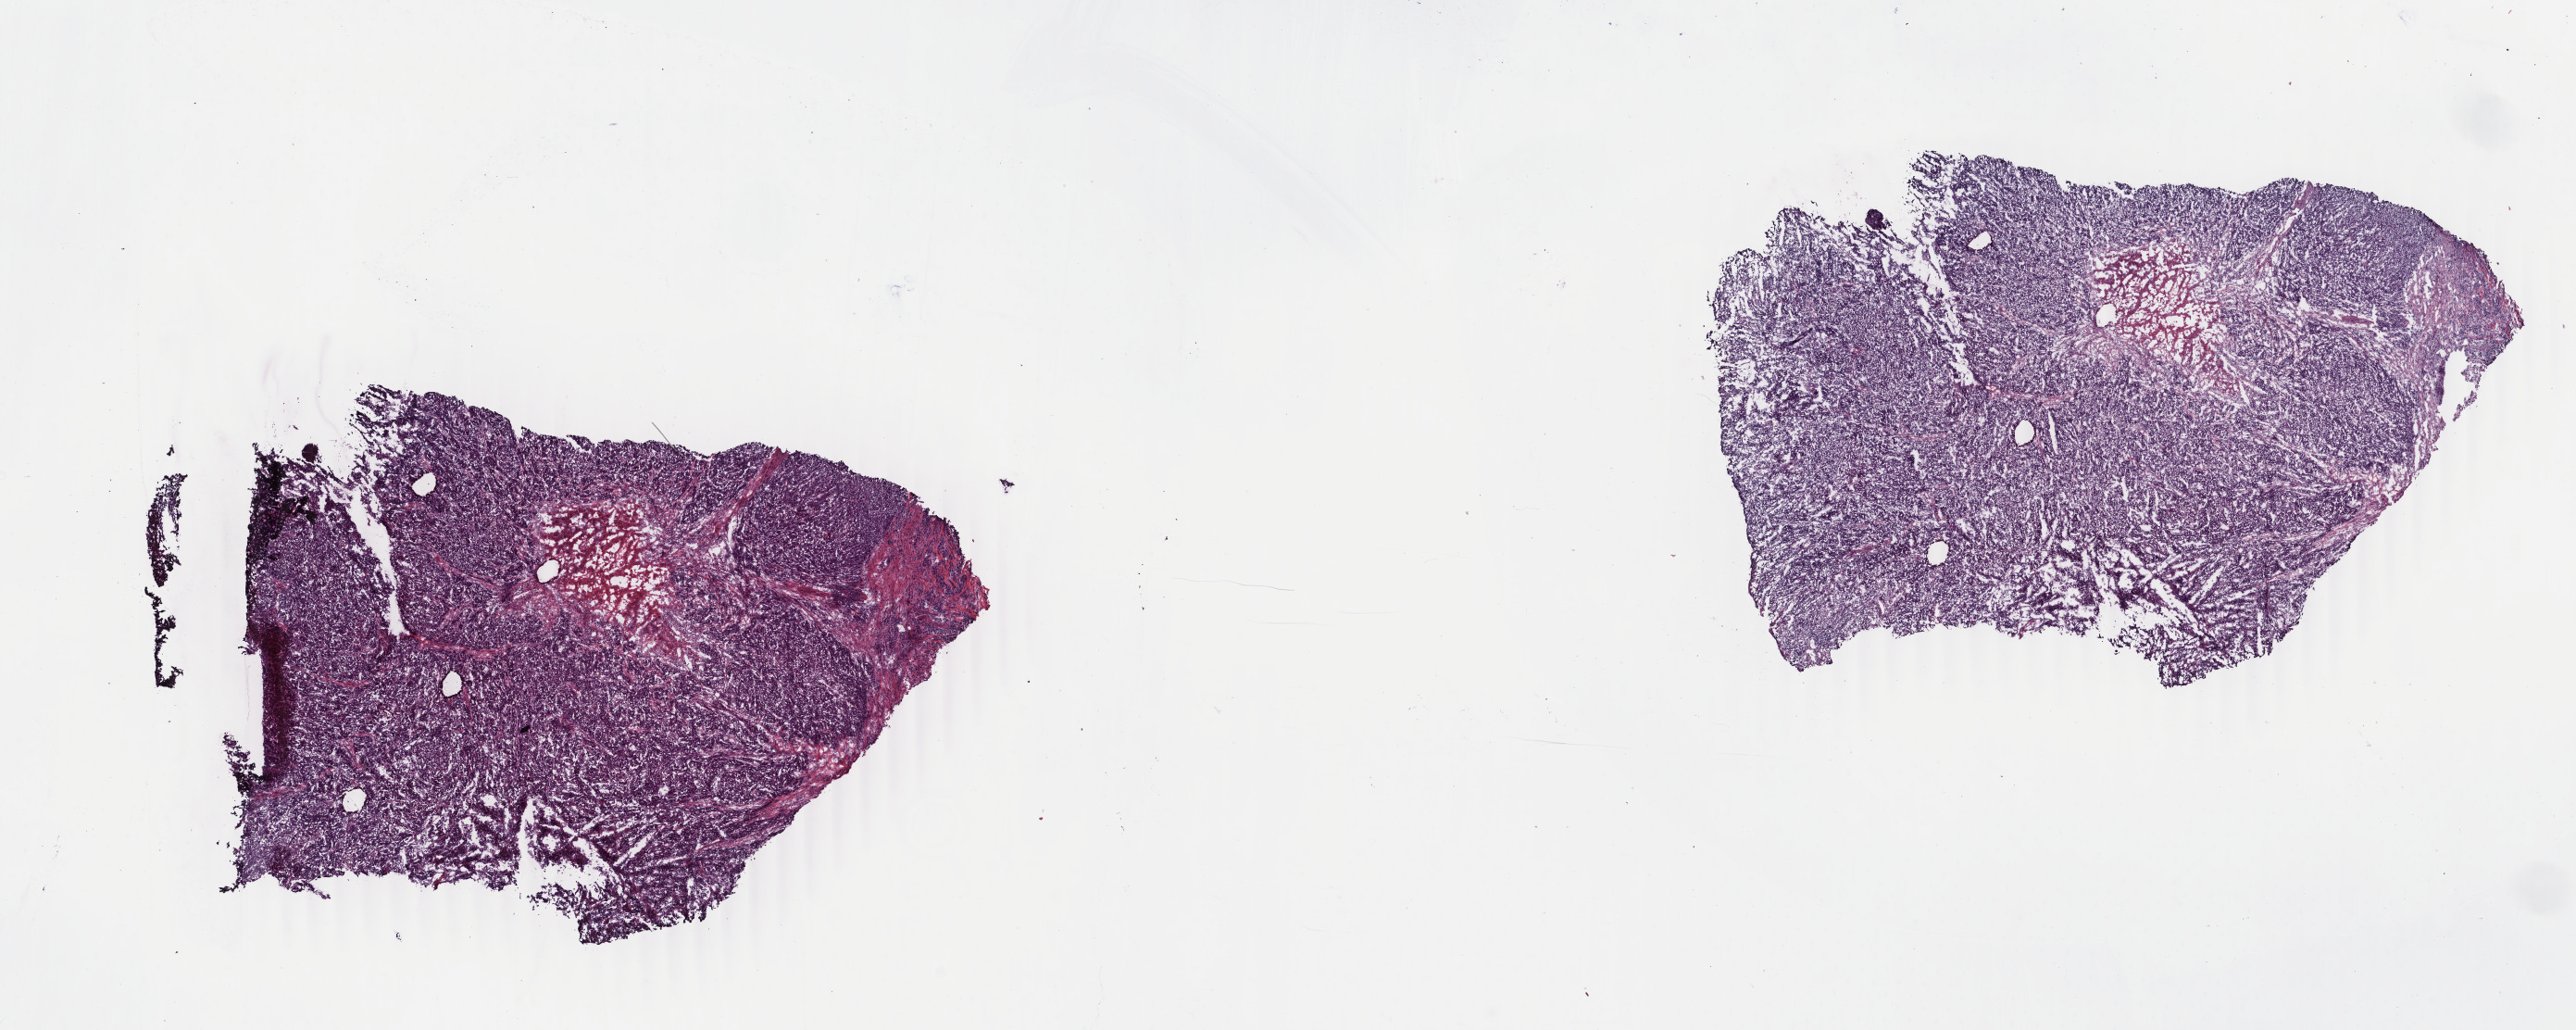
Whole-slide histology image, H&E-stained — a low-resolution overview of the entire scanned area, about 22.1 x 8.8 mm; frozen section from the top of the tissue portion; stomach, primary tumour sample. Male, age 55 years at initial diagnosis. Histologic grade: G3 (poorly differentiated). Composition of this section per pathologist review: tumour cells 93%, tumour nuclei 80%, normal cells 0%, stromal cells 0%, necrosis 7%. Infiltration values recorded for this section: lymphocyte infiltration 2%, monocyte infiltration 1%, neutrophil infiltration 1%.
* pathologic diagnosis: Adenocarcinoma, NOS (fundus of stomach)
* AJCC pathologic stage: IIA (7th edition)